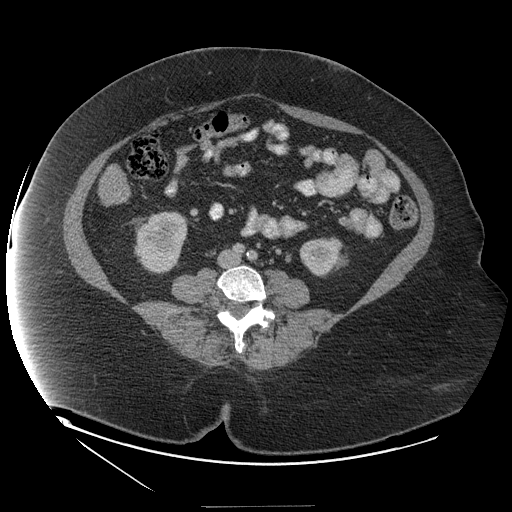
Contrast-enhanced abdominal CT (liver protocol), one axial slice; position 21 of 127 along the scan axis; reconstruction kernel STANDARD; 140 kVp; soft-tissue window (W 400 / L 40 HU); 2.5 mm slice thickness; 512 × 512 image matrix, field of view 480 × 480 mm. From the clinical record (not read from this slice): diagnosis: hepatocellular carcinoma (patient treated with transarterial chemoembolisation; whether this scan precedes or follows treatment is not stated here); TNM stage (as recorded): Stage-II; Child-Pugh class: A; tumour differentiation: well differentiated; tumour nodularity: multinodular.
Structures marked on this image (semi-automatically segmented with operator editing):
- liver parenchyma outside the tumour (the mass and vessels are separate outlines, so this box may not span the whole liver): bounding box (x1, y1, x2, y2) in pixels: (102, 166, 128, 202)